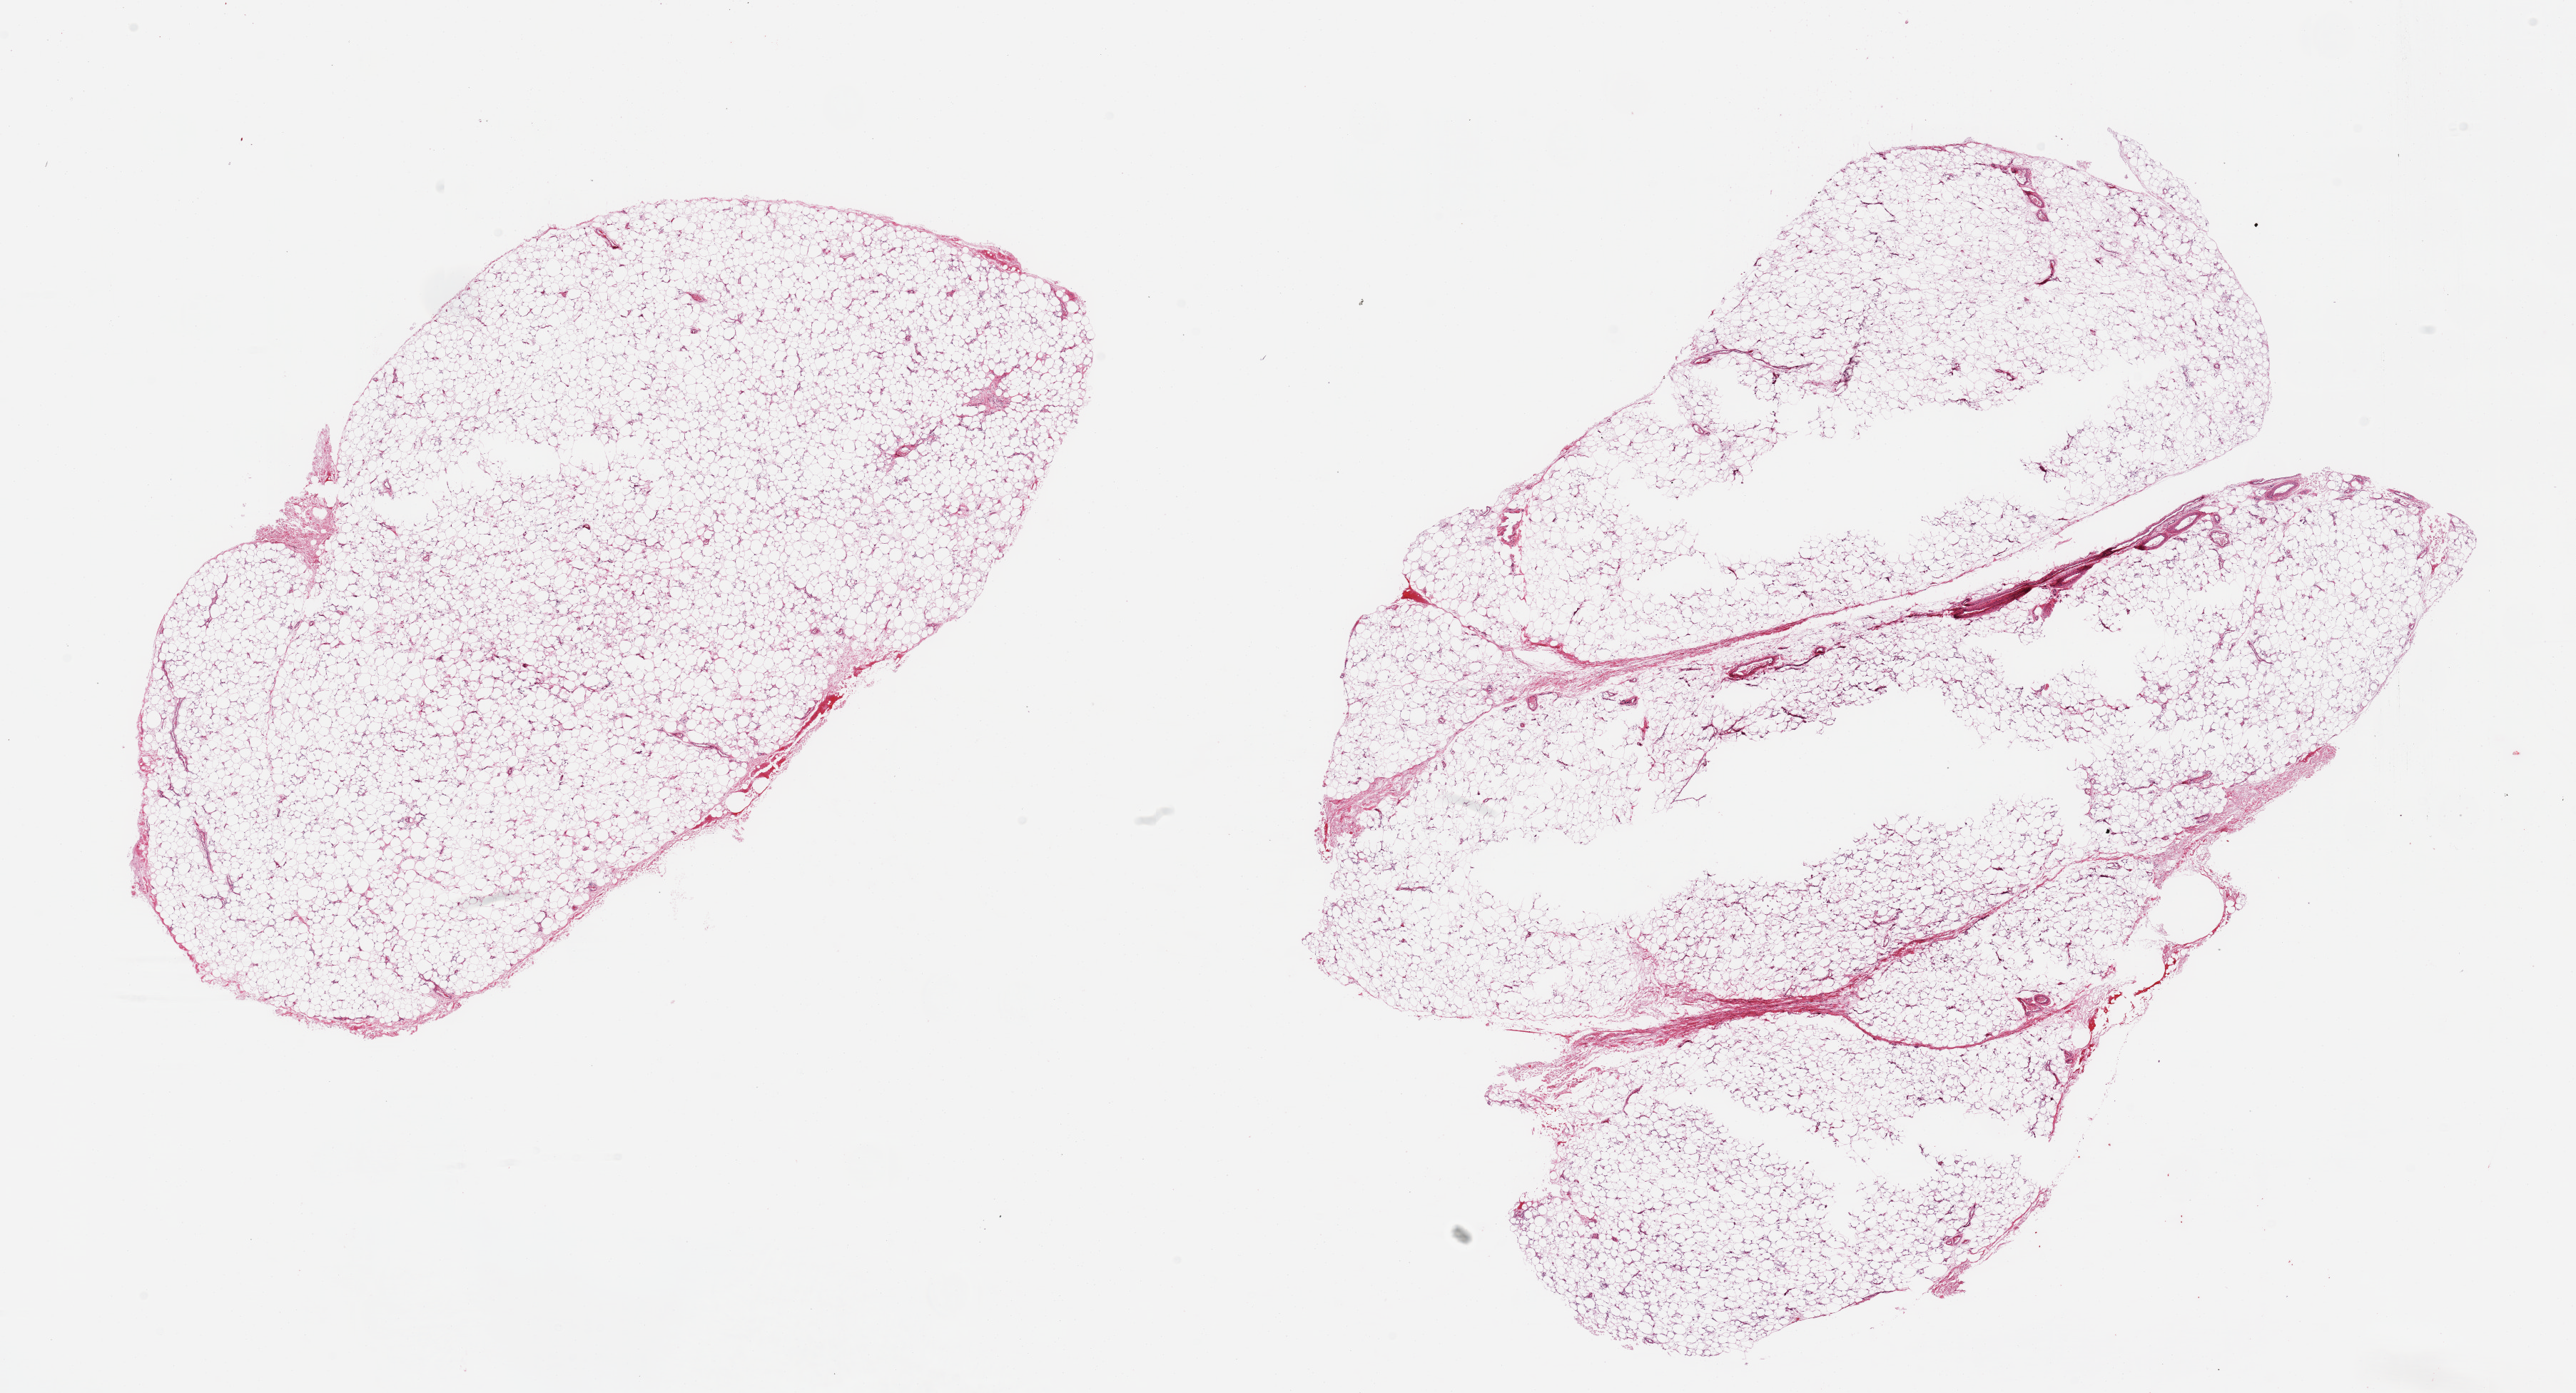
Whole-slide image, haematoxylin and eosin stain, low-resolution overview of the scanned area, about 28.5 x 15.4 mm; PAXgene-fixed, paraffin-embedded tissue; sampled site (target tissue): adipose tissue; tissue donor sample. Donor: male.
Reviewer comment on this tissue sample: 2 pieces; vascular elements and fascia are ~10% of tissue.